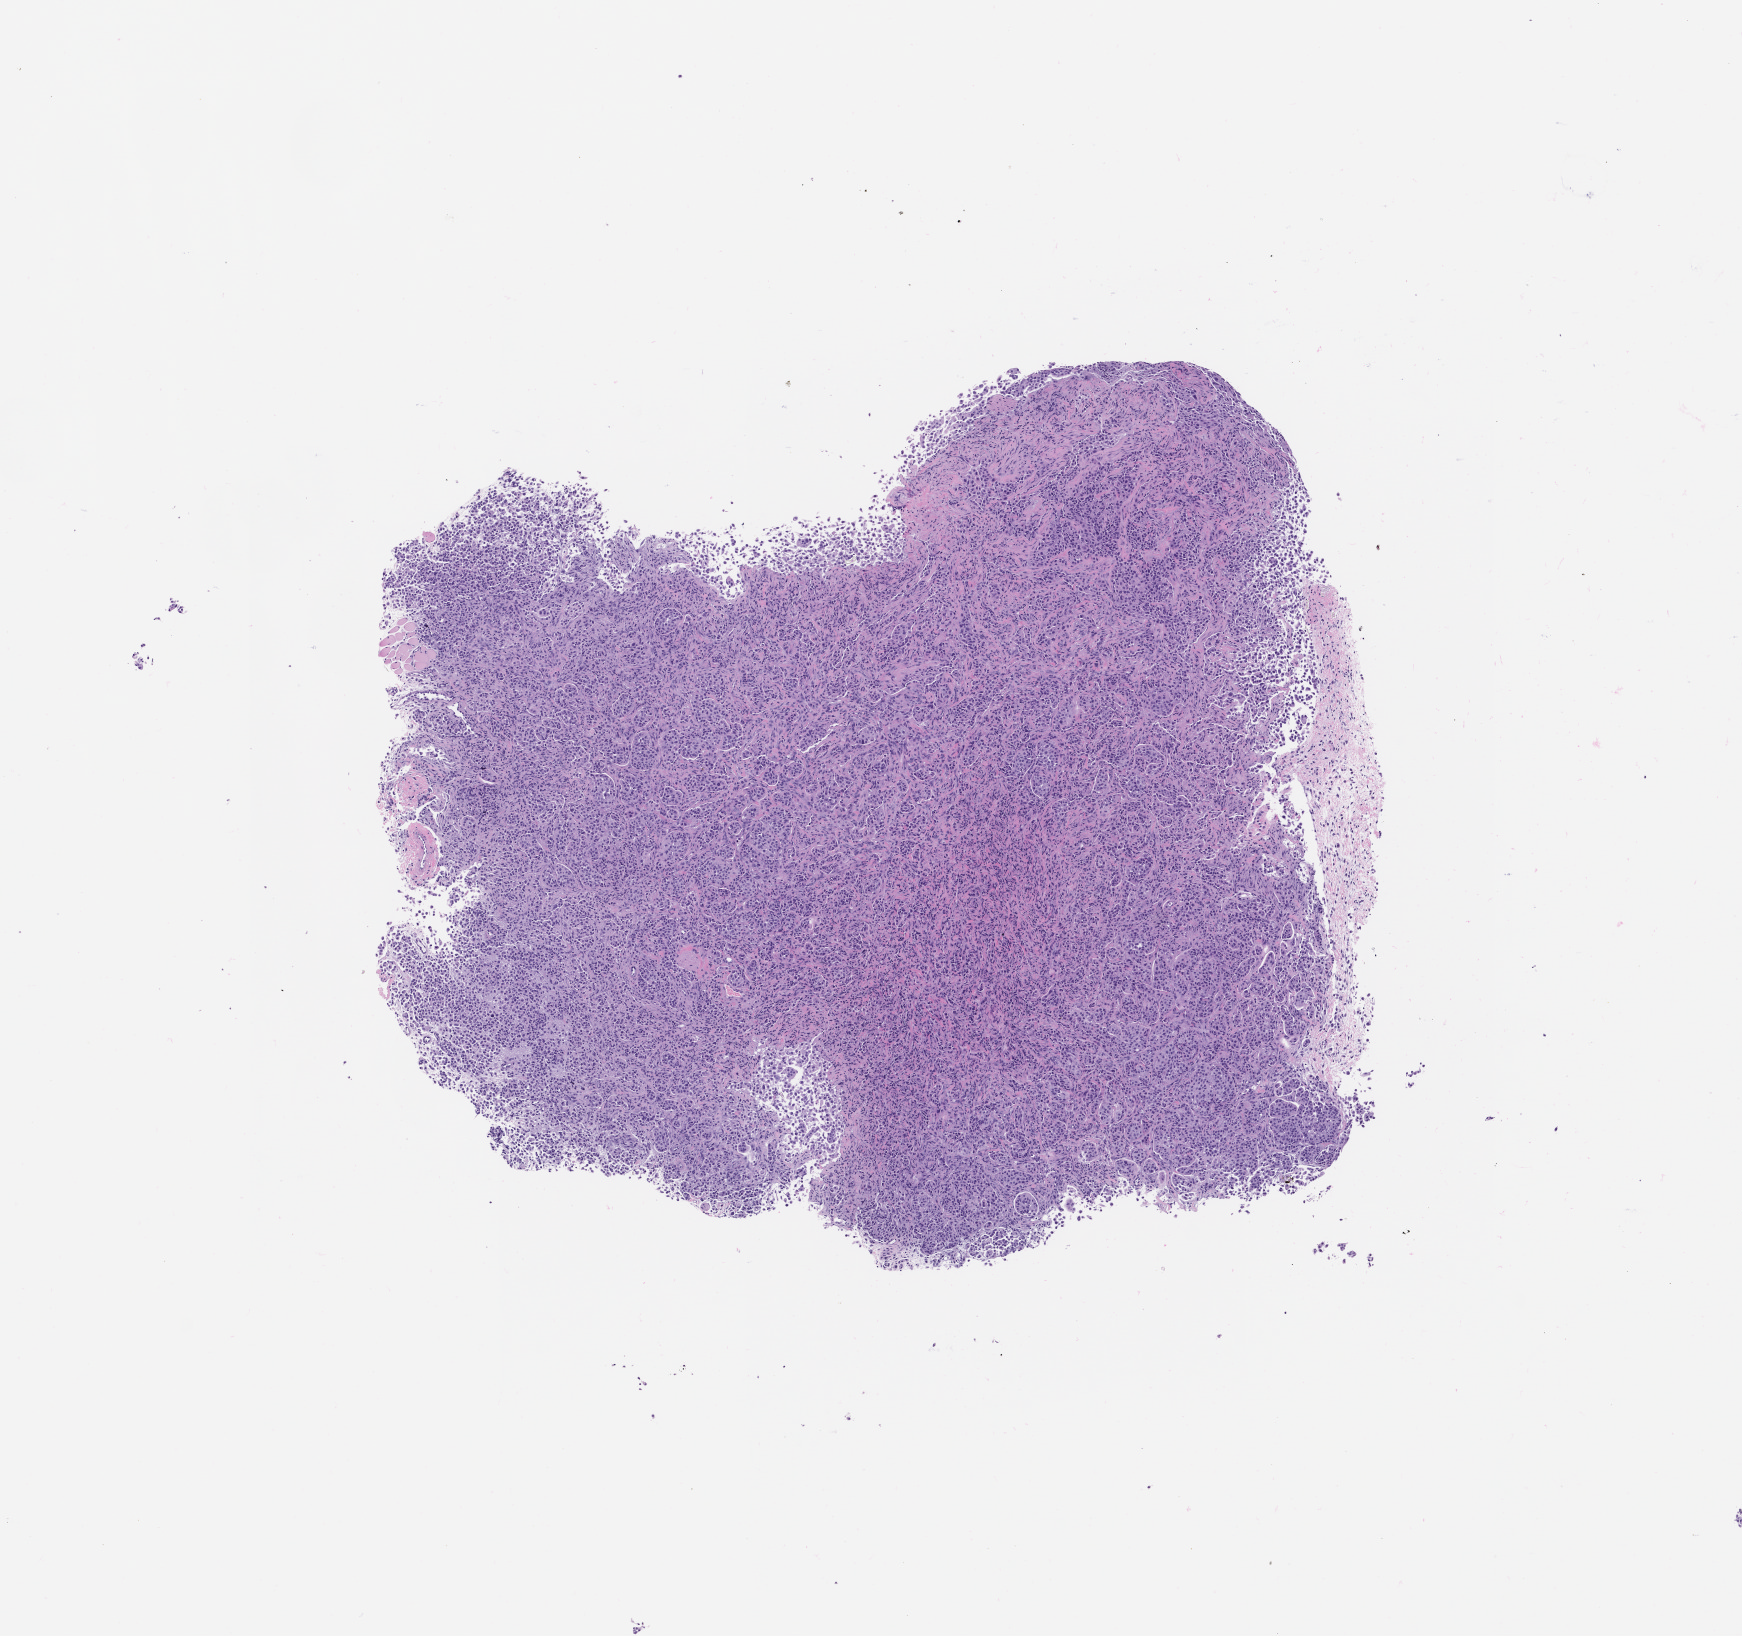
Hematoxylin and eosin (H&E) whole-slide image of a patient-derived xenograft (PDX) tumor grown in a mouse, passage 1, a low-resolution overview of the entire scanned area, about 7.0 x 6.6 mm; formalin-fixed, paraffin-embedded (FFPE) tissue; tumor site category: bladder.
Originating patient diagnosis: Transitional Cell Carcinoma.